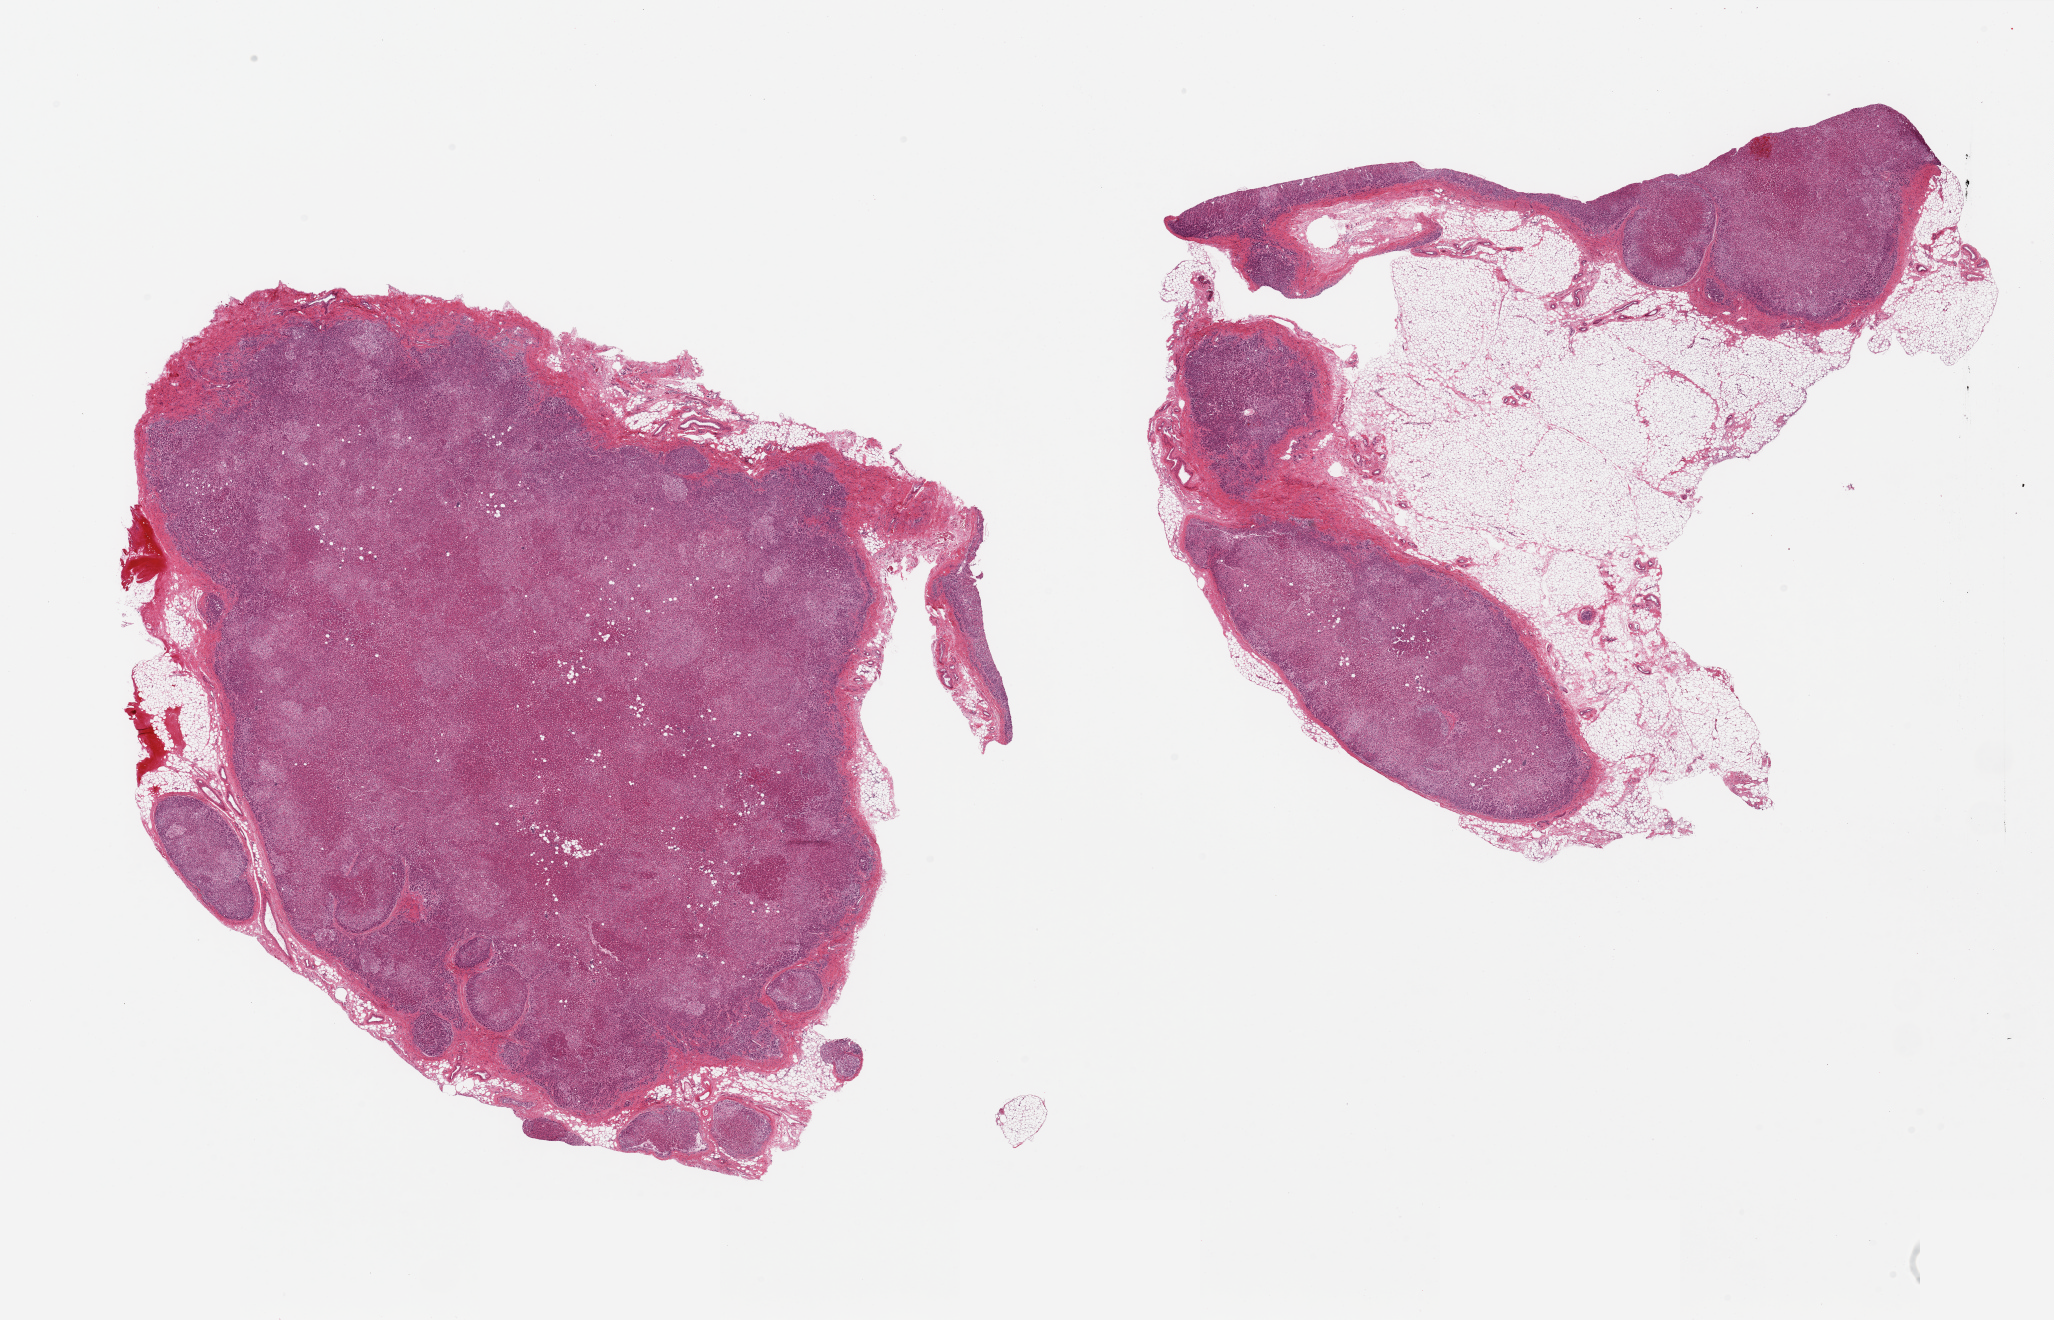
Digitized hematoxylin and eosin (H&E)-stained section, brightfield — shown as a low-resolution overview of the whole scanned area (about 32.5 x 20.9 mm). PAXgene-fixed paraffin-embedded (PFPE) section. Target tissue: adrenal gland. Donor tissue sample. Female donor.
Review note (as recorded): 2 pieces, cortex, adherent fat is ~ 30% tissue.